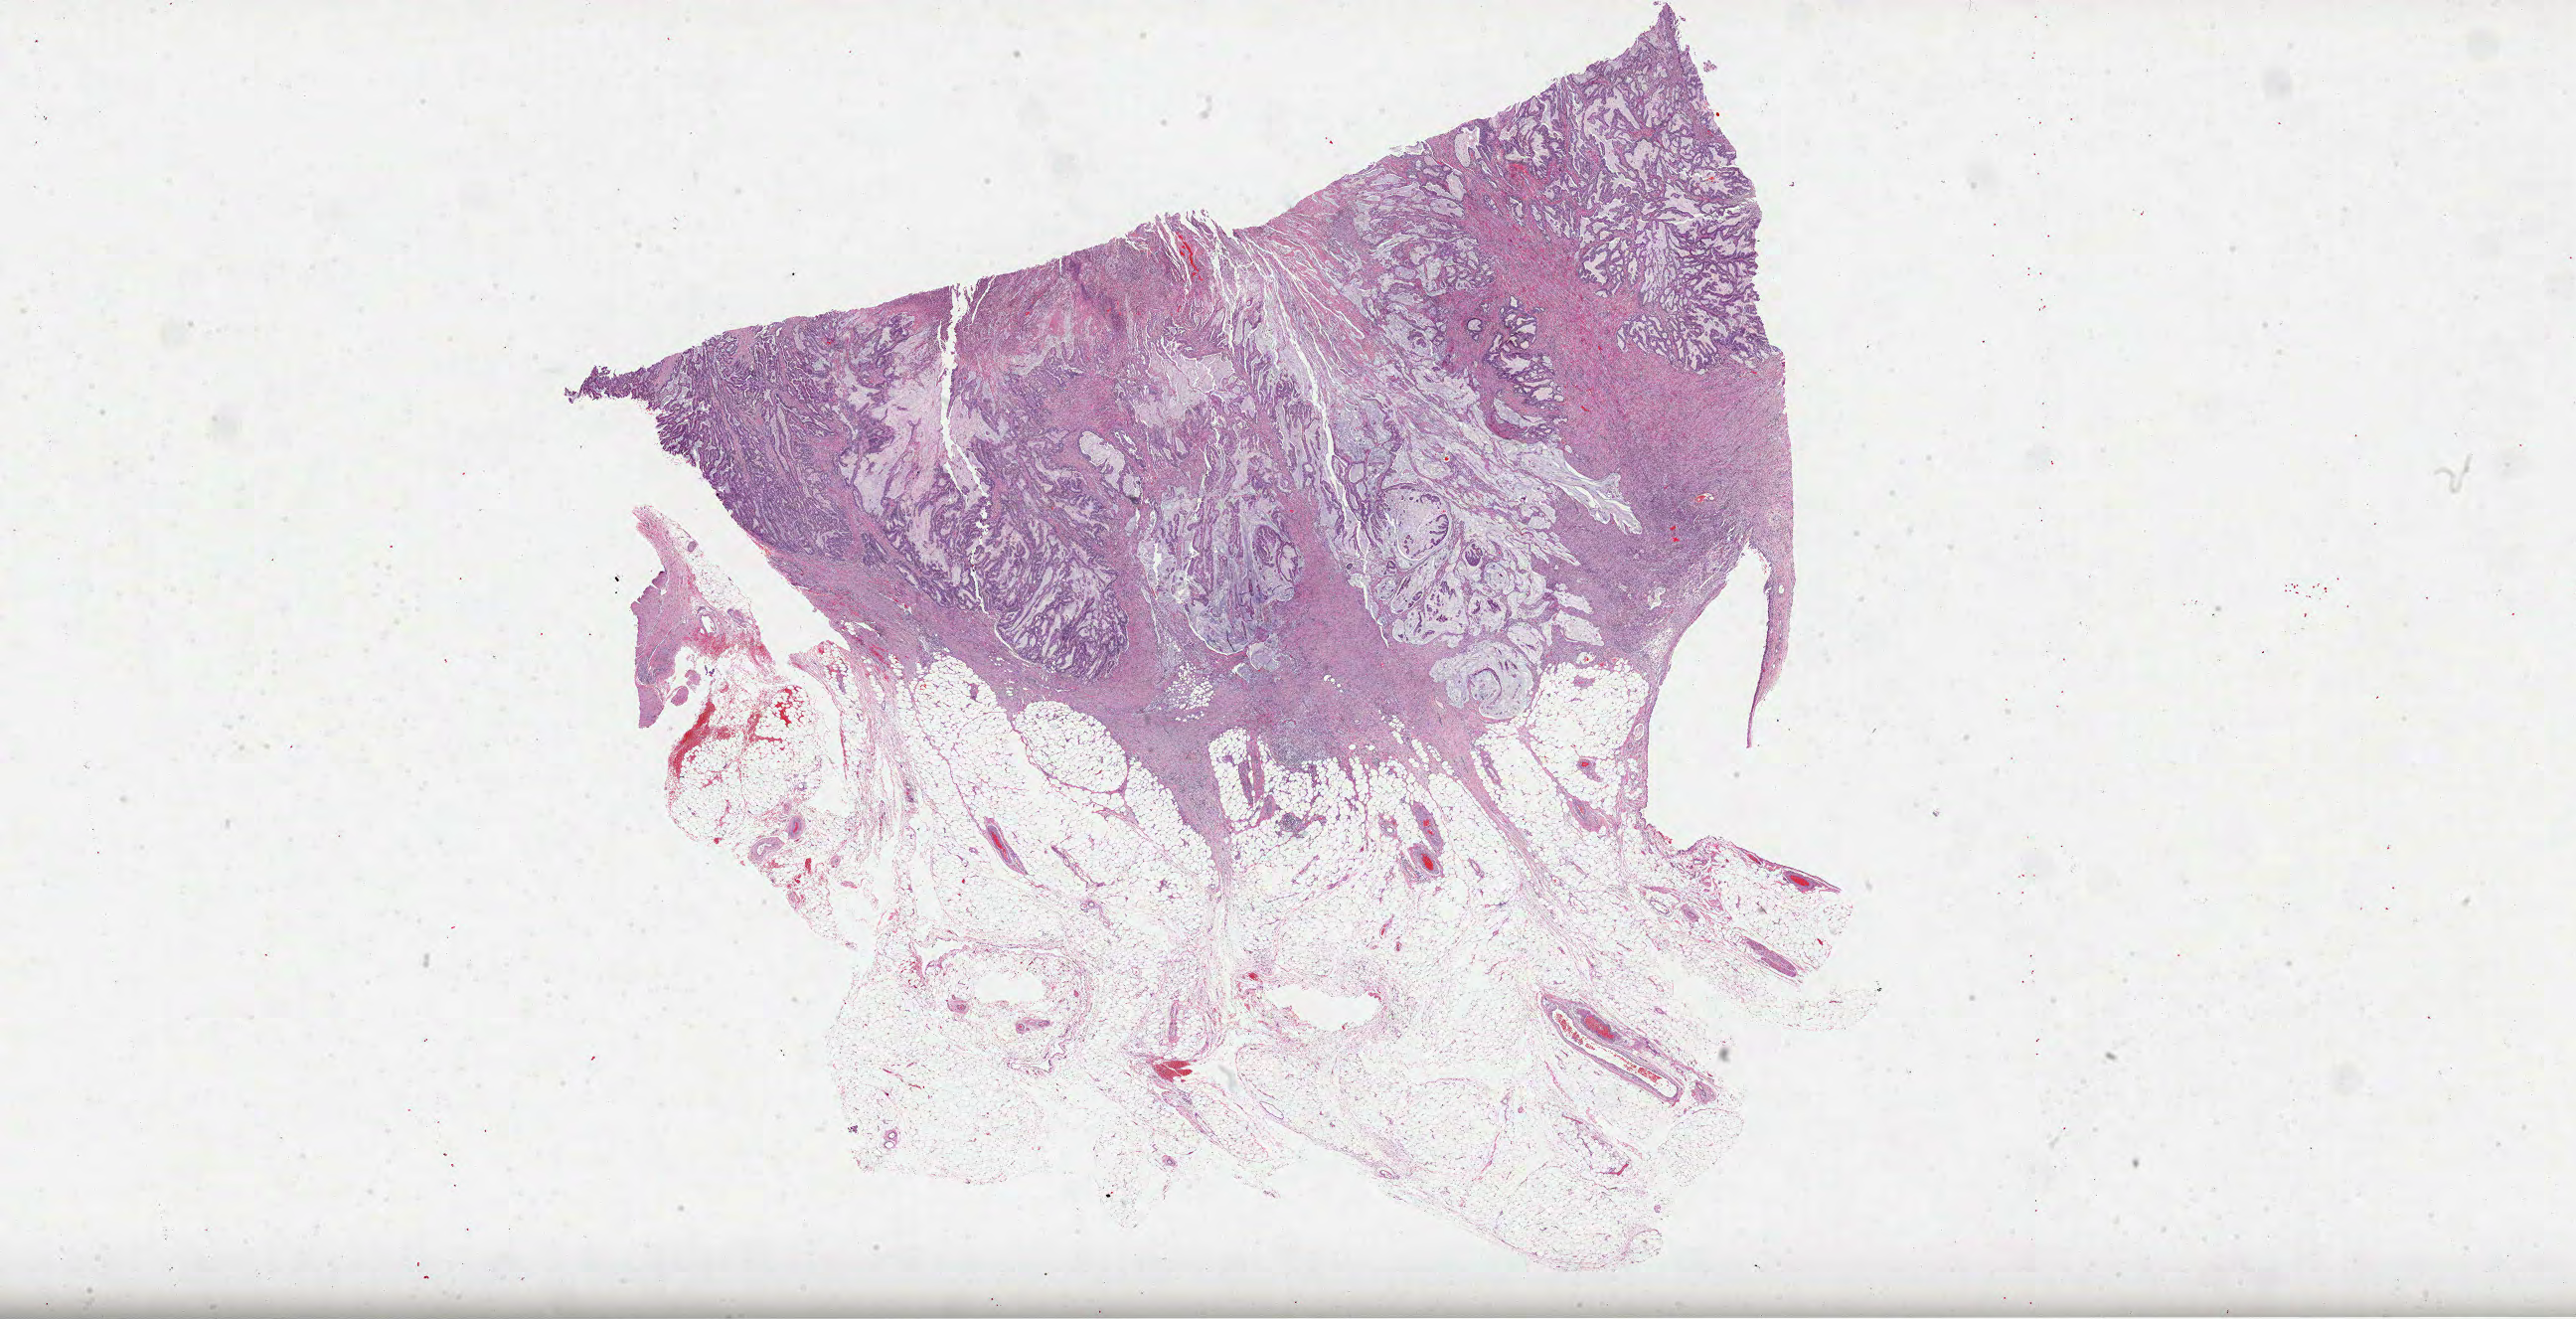
Hematoxylin and eosin (H&E) stained whole-slide image — low-resolution overview of the scanned area, about 41.8 x 21.4 mm. FFPE section. Colon, primary tumour sample. Female, age 63 years at initial diagnosis.
- histologic diagnosis: Adenocarcinoma, NOS
- TNM: T3 N0 M0
- AJCC pathologic stage: IIA (7th edition)